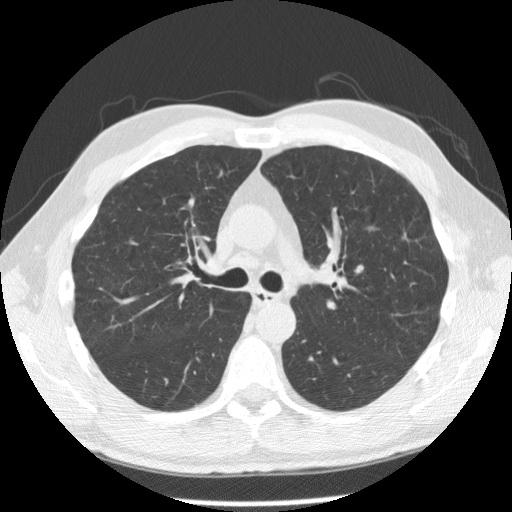
Axial slice from a low-dose chest CT screening exam; second screening round (one year after baseline); lung window (W 1500 / L -600 HU); 2.5 mm slice thickness; slice 122 of 181 in the series. Male participant, aged 55 years at enrolment. Current smoker at enrolment.
Expert-annotated lung lesion, bounding box [x1, y1, x2, y2] px = [333, 250, 375, 293]. Screening reader's record for this exam: no non-calcified nodule ≥4 mm recorded. Official screen result: negative screen, minor abnormalities not suspicious for lung cancer. Later outcome: lung cancer diagnosed 356 days after this screen (after the third annual screen) — small cell carcinoma, NOS, left upper lobe, undifferentiated (G4), stage IV (AJCC 6th edition), 60 mm at pathology.